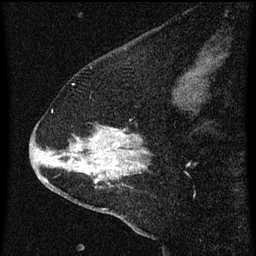
Breast MRI (dynamic contrast-enhanced), one sagittal slice; slice 17 of 60 in the series (ordered by position); dynamic contrast-enhanced series, image 2 of 3 at this slice position (ordered by acquisition); 1.5 T; TE 4.2 ms, TR 8 ms; 256 × 256 image matrix, field of view 180 × 180 mm. Patient: female, 47 years.
Outlined on this slice (semi-automatic segmentation, software-assisted and operator-edited):
- analysis volume of interest (the breast-tissue region the enhancement analysis was run in; not a lesion): bounding box (x1, y1, x2, y2) in pixels: (36, 110, 152, 213)
- tumour enhancement mask (voxels above the 70 % enhancement threshold inside the analysis volume of interest): (41, 130, 146, 183)